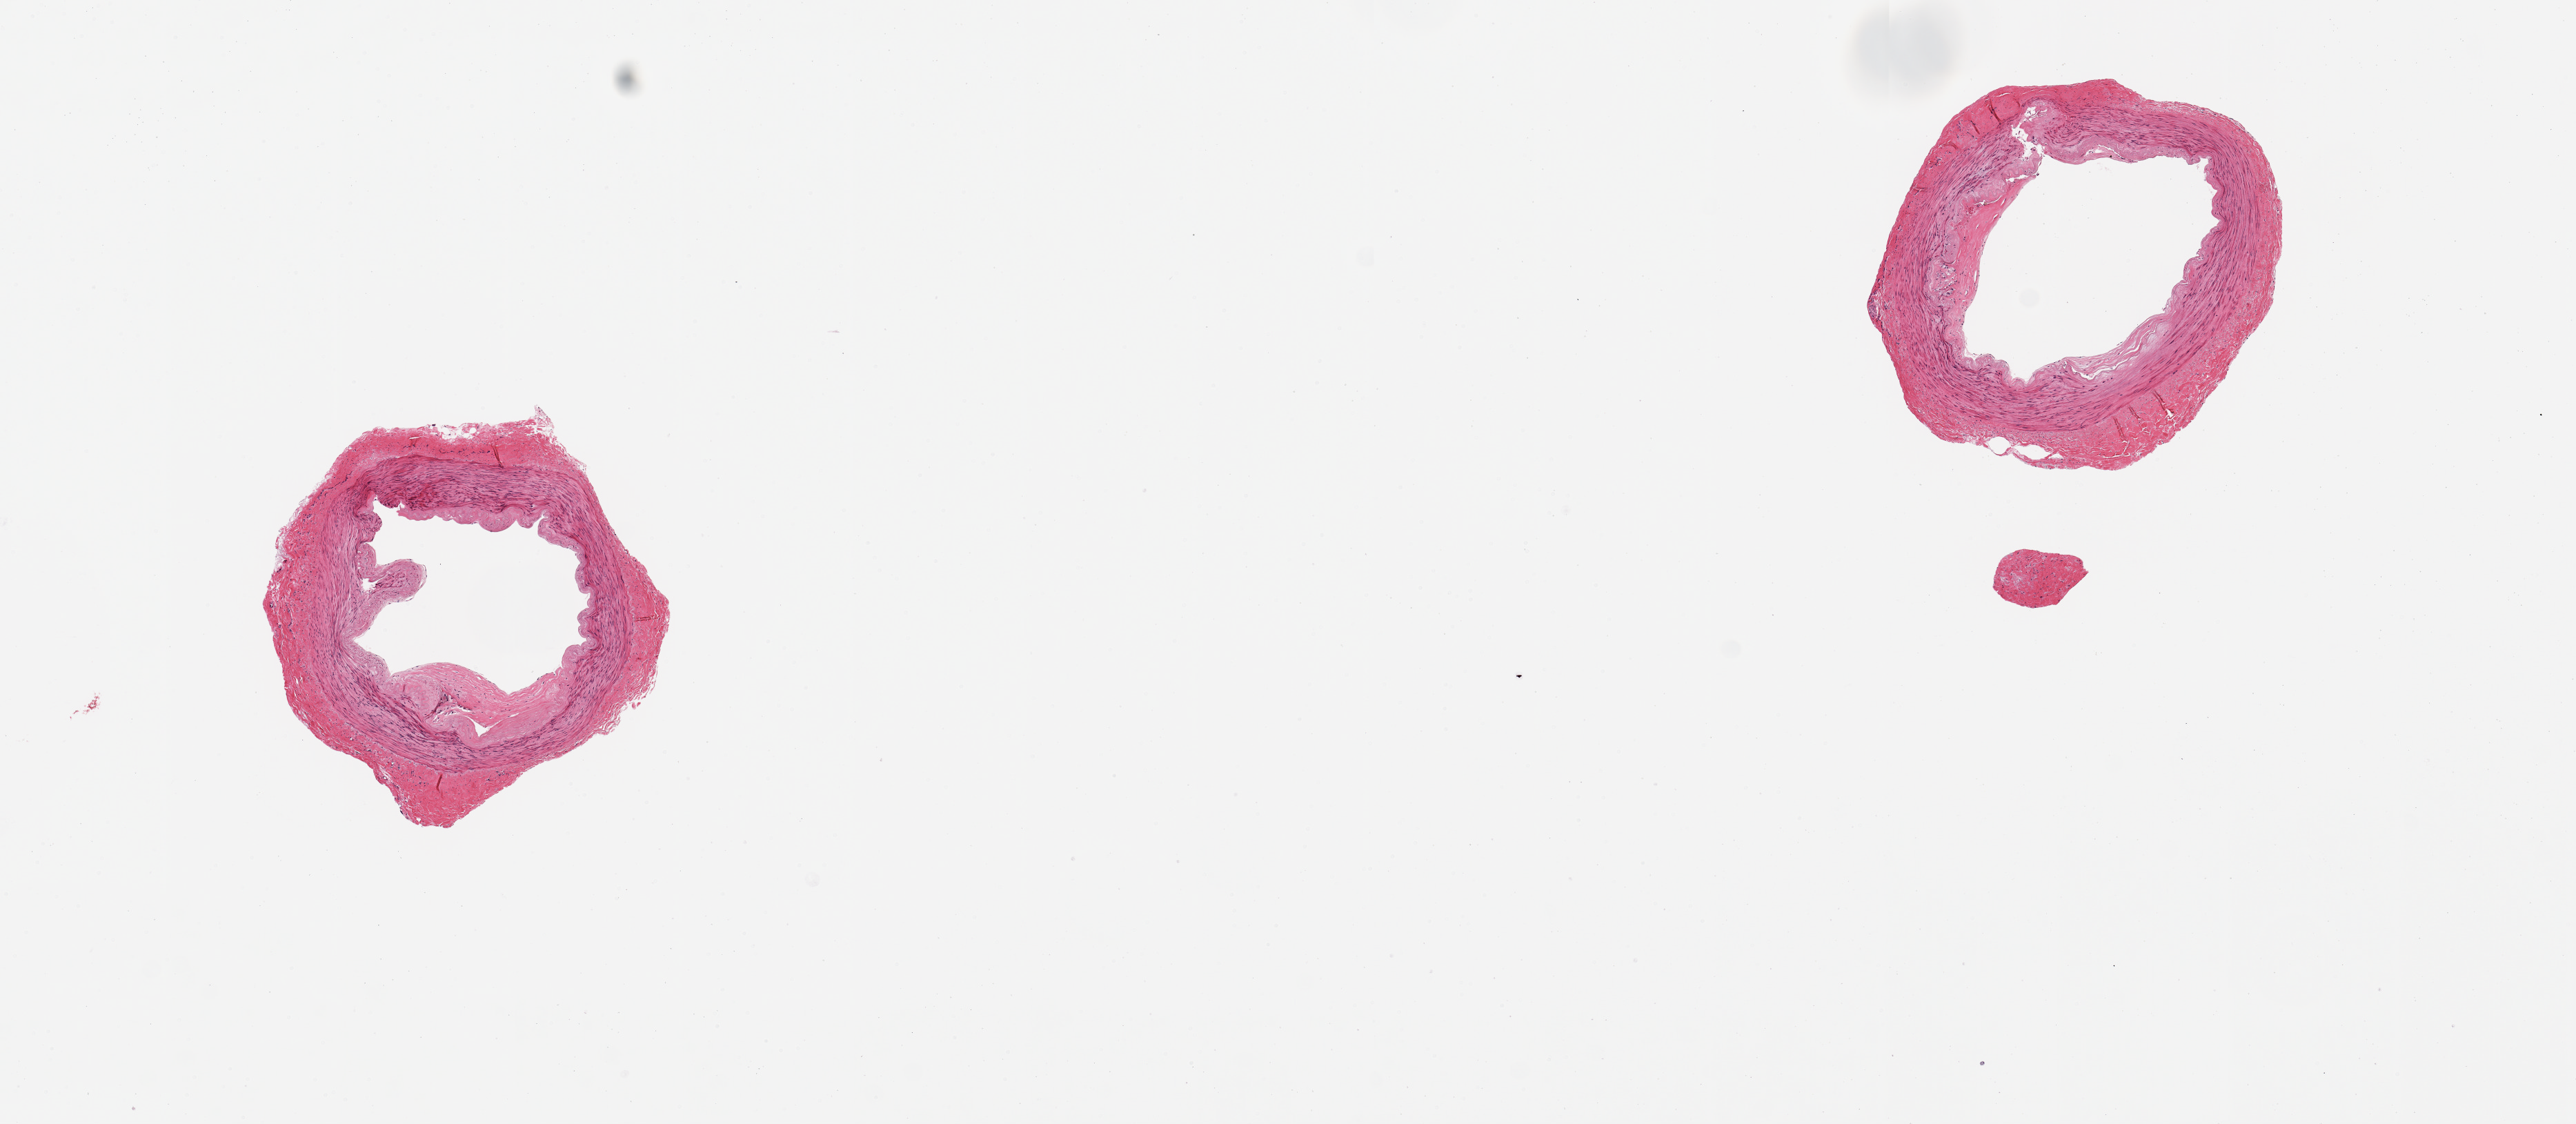
H&E whole-slide image, brightfield, whole scanned area (about 14.8 x 6.4 mm, slide scanned at 20x) shown as a low-resolution overview, PAXgene-fixed, paraffin-embedded tissue, sampled site (target tissue): tibial artery, donor tissue sample. Donor sex: female.
Review note (as recorded): 2 pieces. 2x2 & 2.5x2mm; well trimmed of adipose.